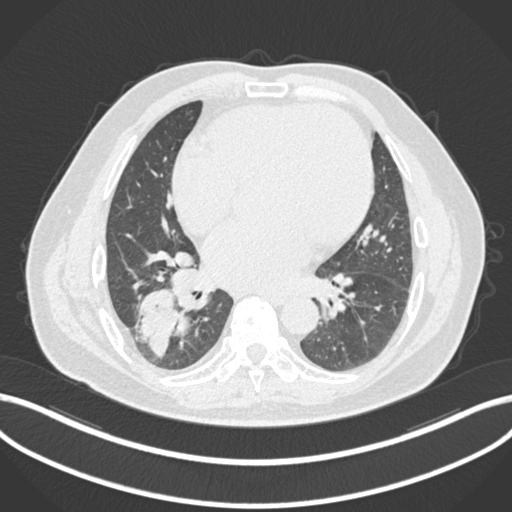
Chest CT, one axial slice. Position 76 of 200 along the scan axis. Lung window (W 1500 / L -600 HU). 1 mm slice thickness. 512 × 512 image matrix. Patient: male, 59 years.
Annotated regions visible in this slice (bounding box drawn by a radiologist):
- lung tumour (recorded histology: adenocarcinoma): bounding box <135,287,189,358> (left, top, right, bottom; pixels)